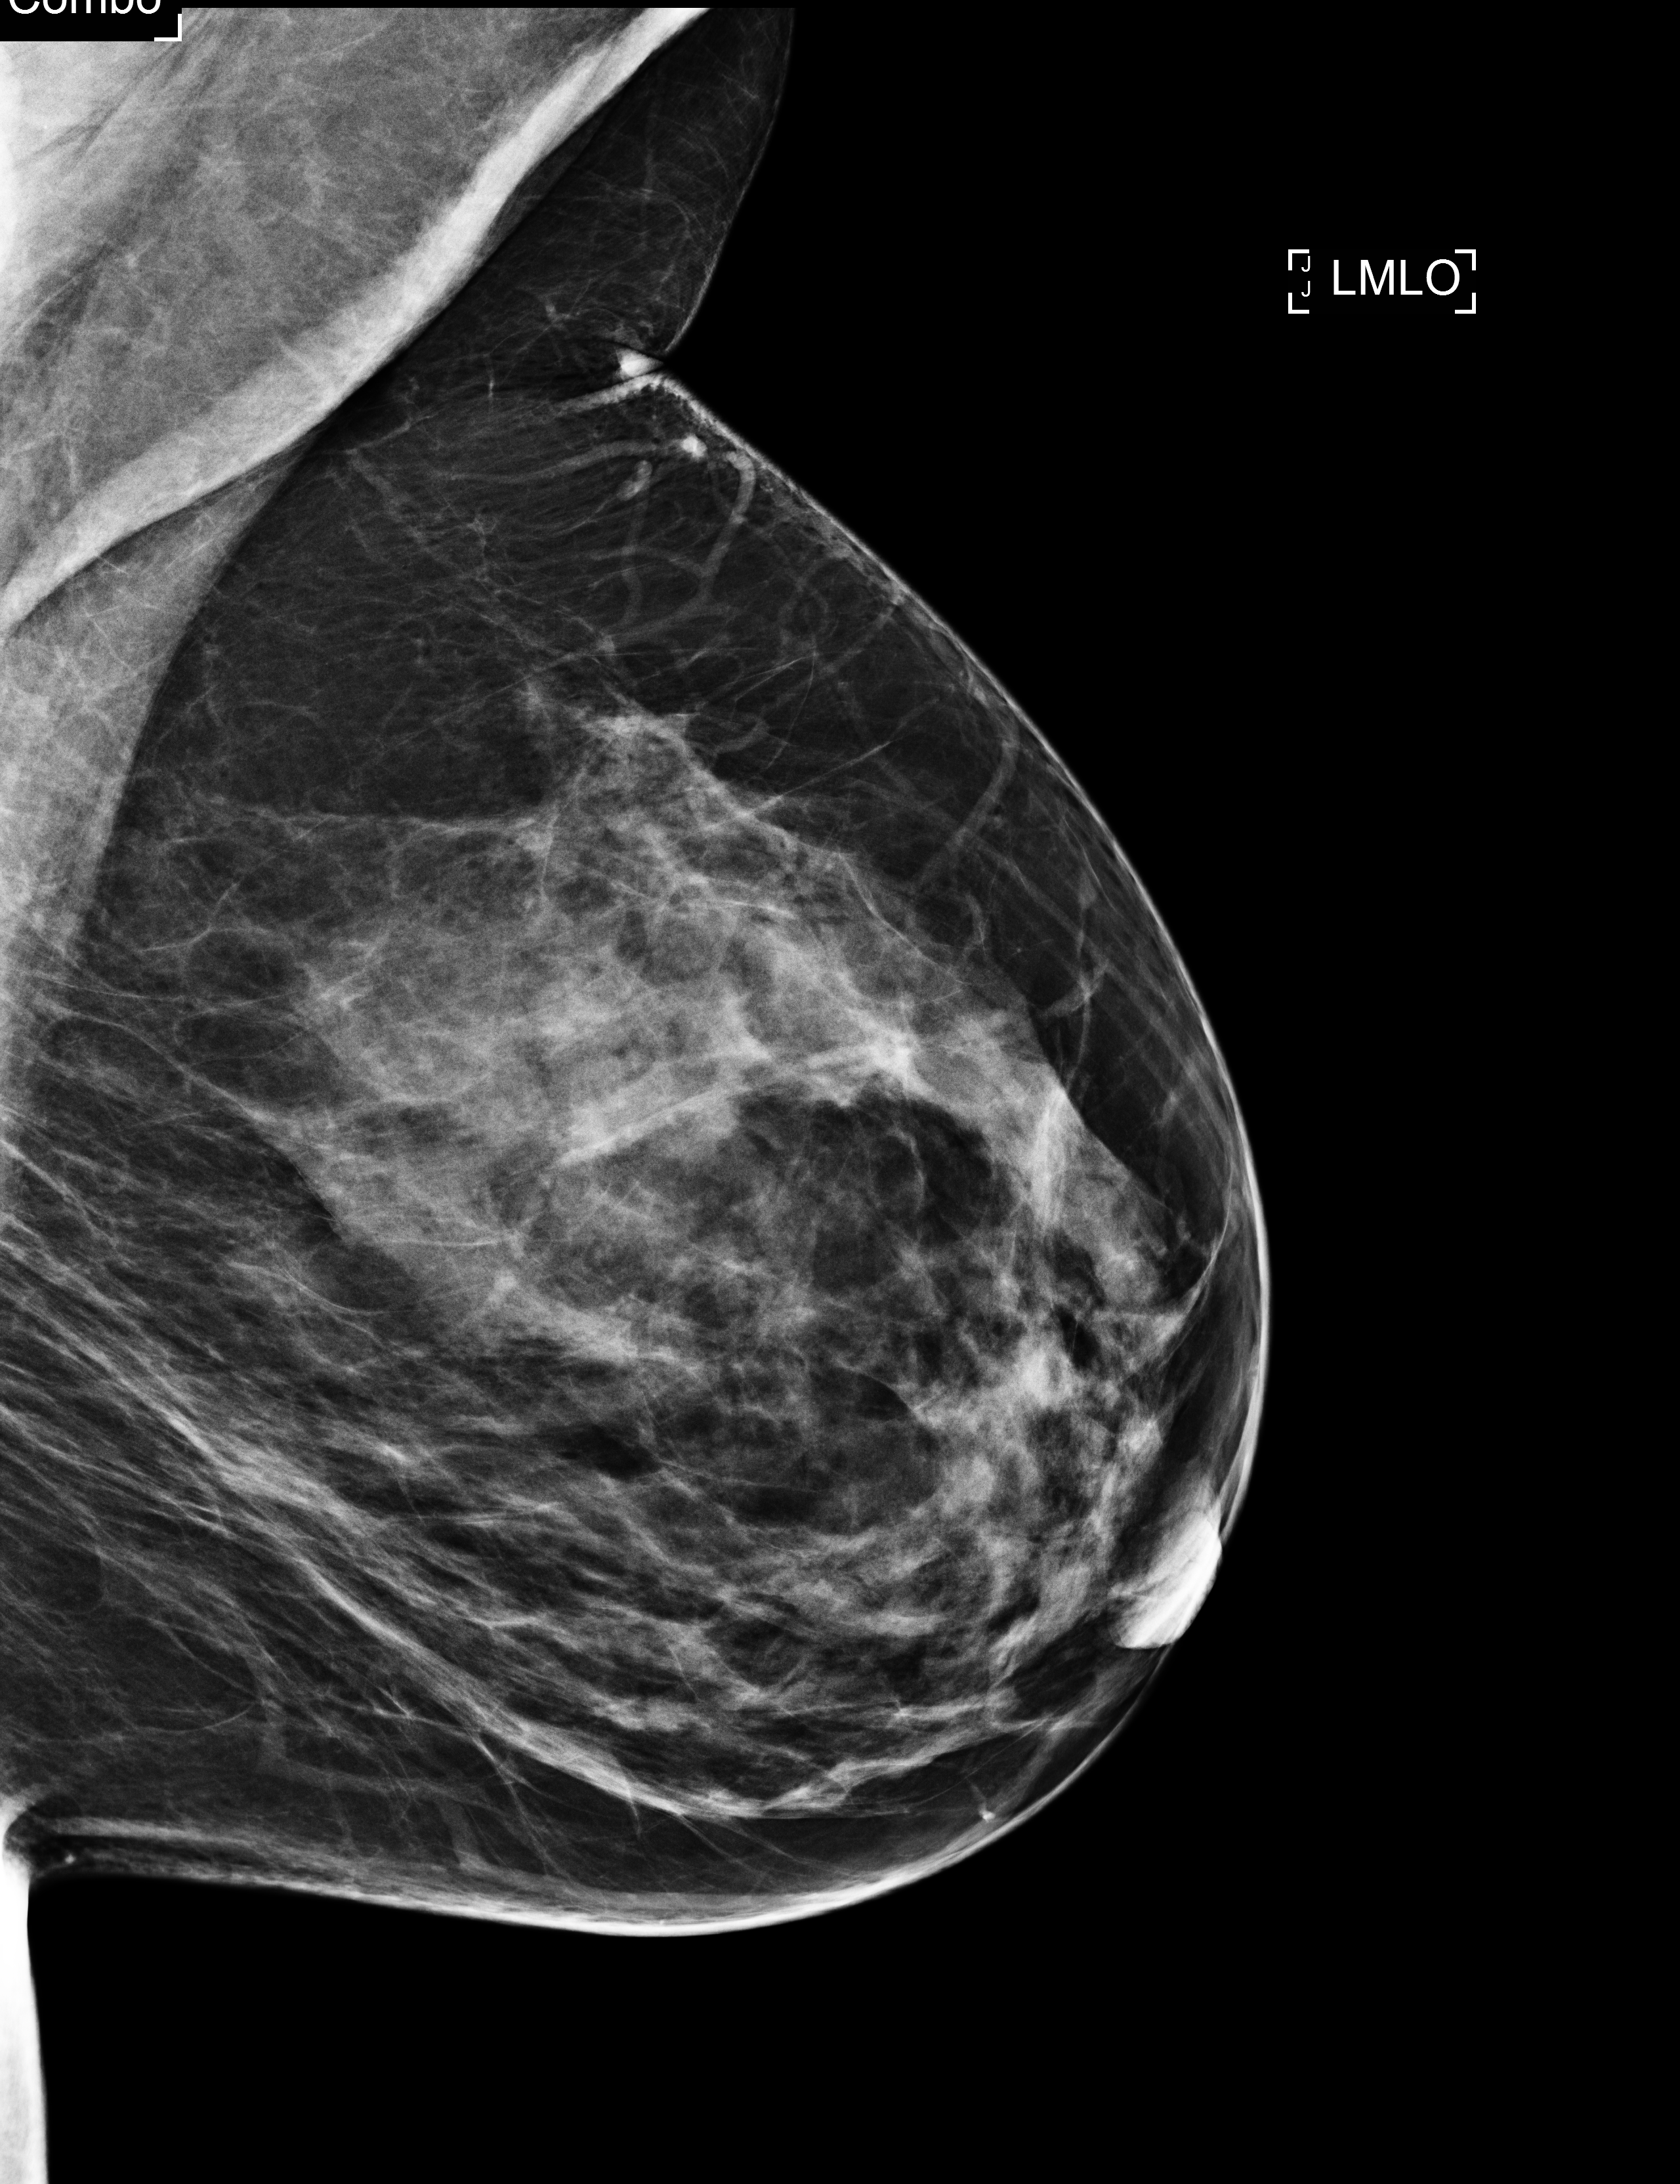
Annual screening mammography examination, system: Selenia Dimensions. Patient aged 41 years (female).
Image type: full-field digital mammogram. Breast: left. Projection: MLO view. BI-RADS breast density category at the screening exam (both breasts, scale 1–4): 3. Final BI-RADS category for the screening round (tomosynthesis exam, both breasts): category 1. Recall: recalled for additional imaging after this screen.